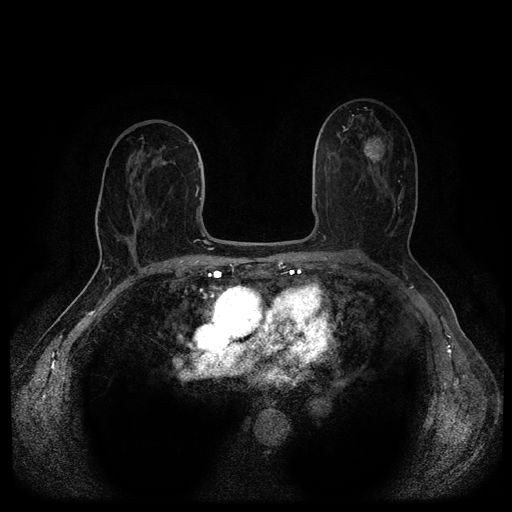
Breast MRI (dynamic contrast-enhanced, multi-phase), one axial slice; slice 57 of 116 in the series (ordered by position); dynamic contrast-enhanced series, time point 2 of 5 at this slice position (early post-contrast); 1.5 T; TE 2.6 ms, TR 5.4 ms; 512 × 512 image matrix, field of view 340 × 340 mm. Patient: female, 69 years.
Outlined on this slice (semi-automatic segmentation, software-assisted and operator-edited):
- breast lesion (labelled benign in the annotation): box from (x=361, y=135) to (x=385, y=171) px